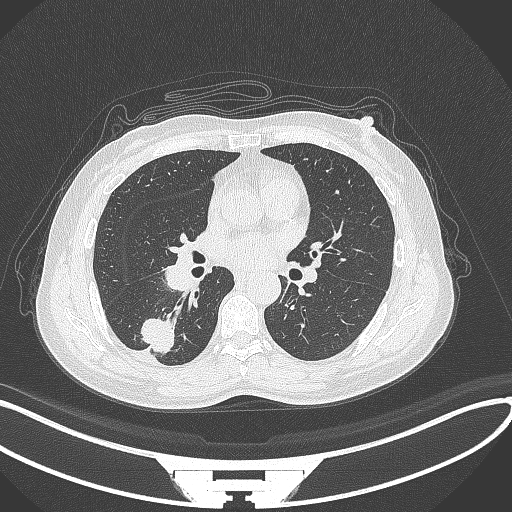
Chest CT, one axial slice. Slice 154 of 352 in the series (ordered by position). 120 kVp. Lung window (W 1500 / L -600 HU). 1 mm slice thickness. 512 × 512 image matrix, field of view 400 × 400 mm. Female patient, age 55 years. From the clinical record (not read from this slice): clinical TNM (as recorded): T1c N1 M0.
Outlined on this slice (rectangle marked by the reading radiologist):
- lung tumour (recorded histology: adenocarcinoma): bounding box <137,310,180,355> (left, top, right, bottom; pixels)